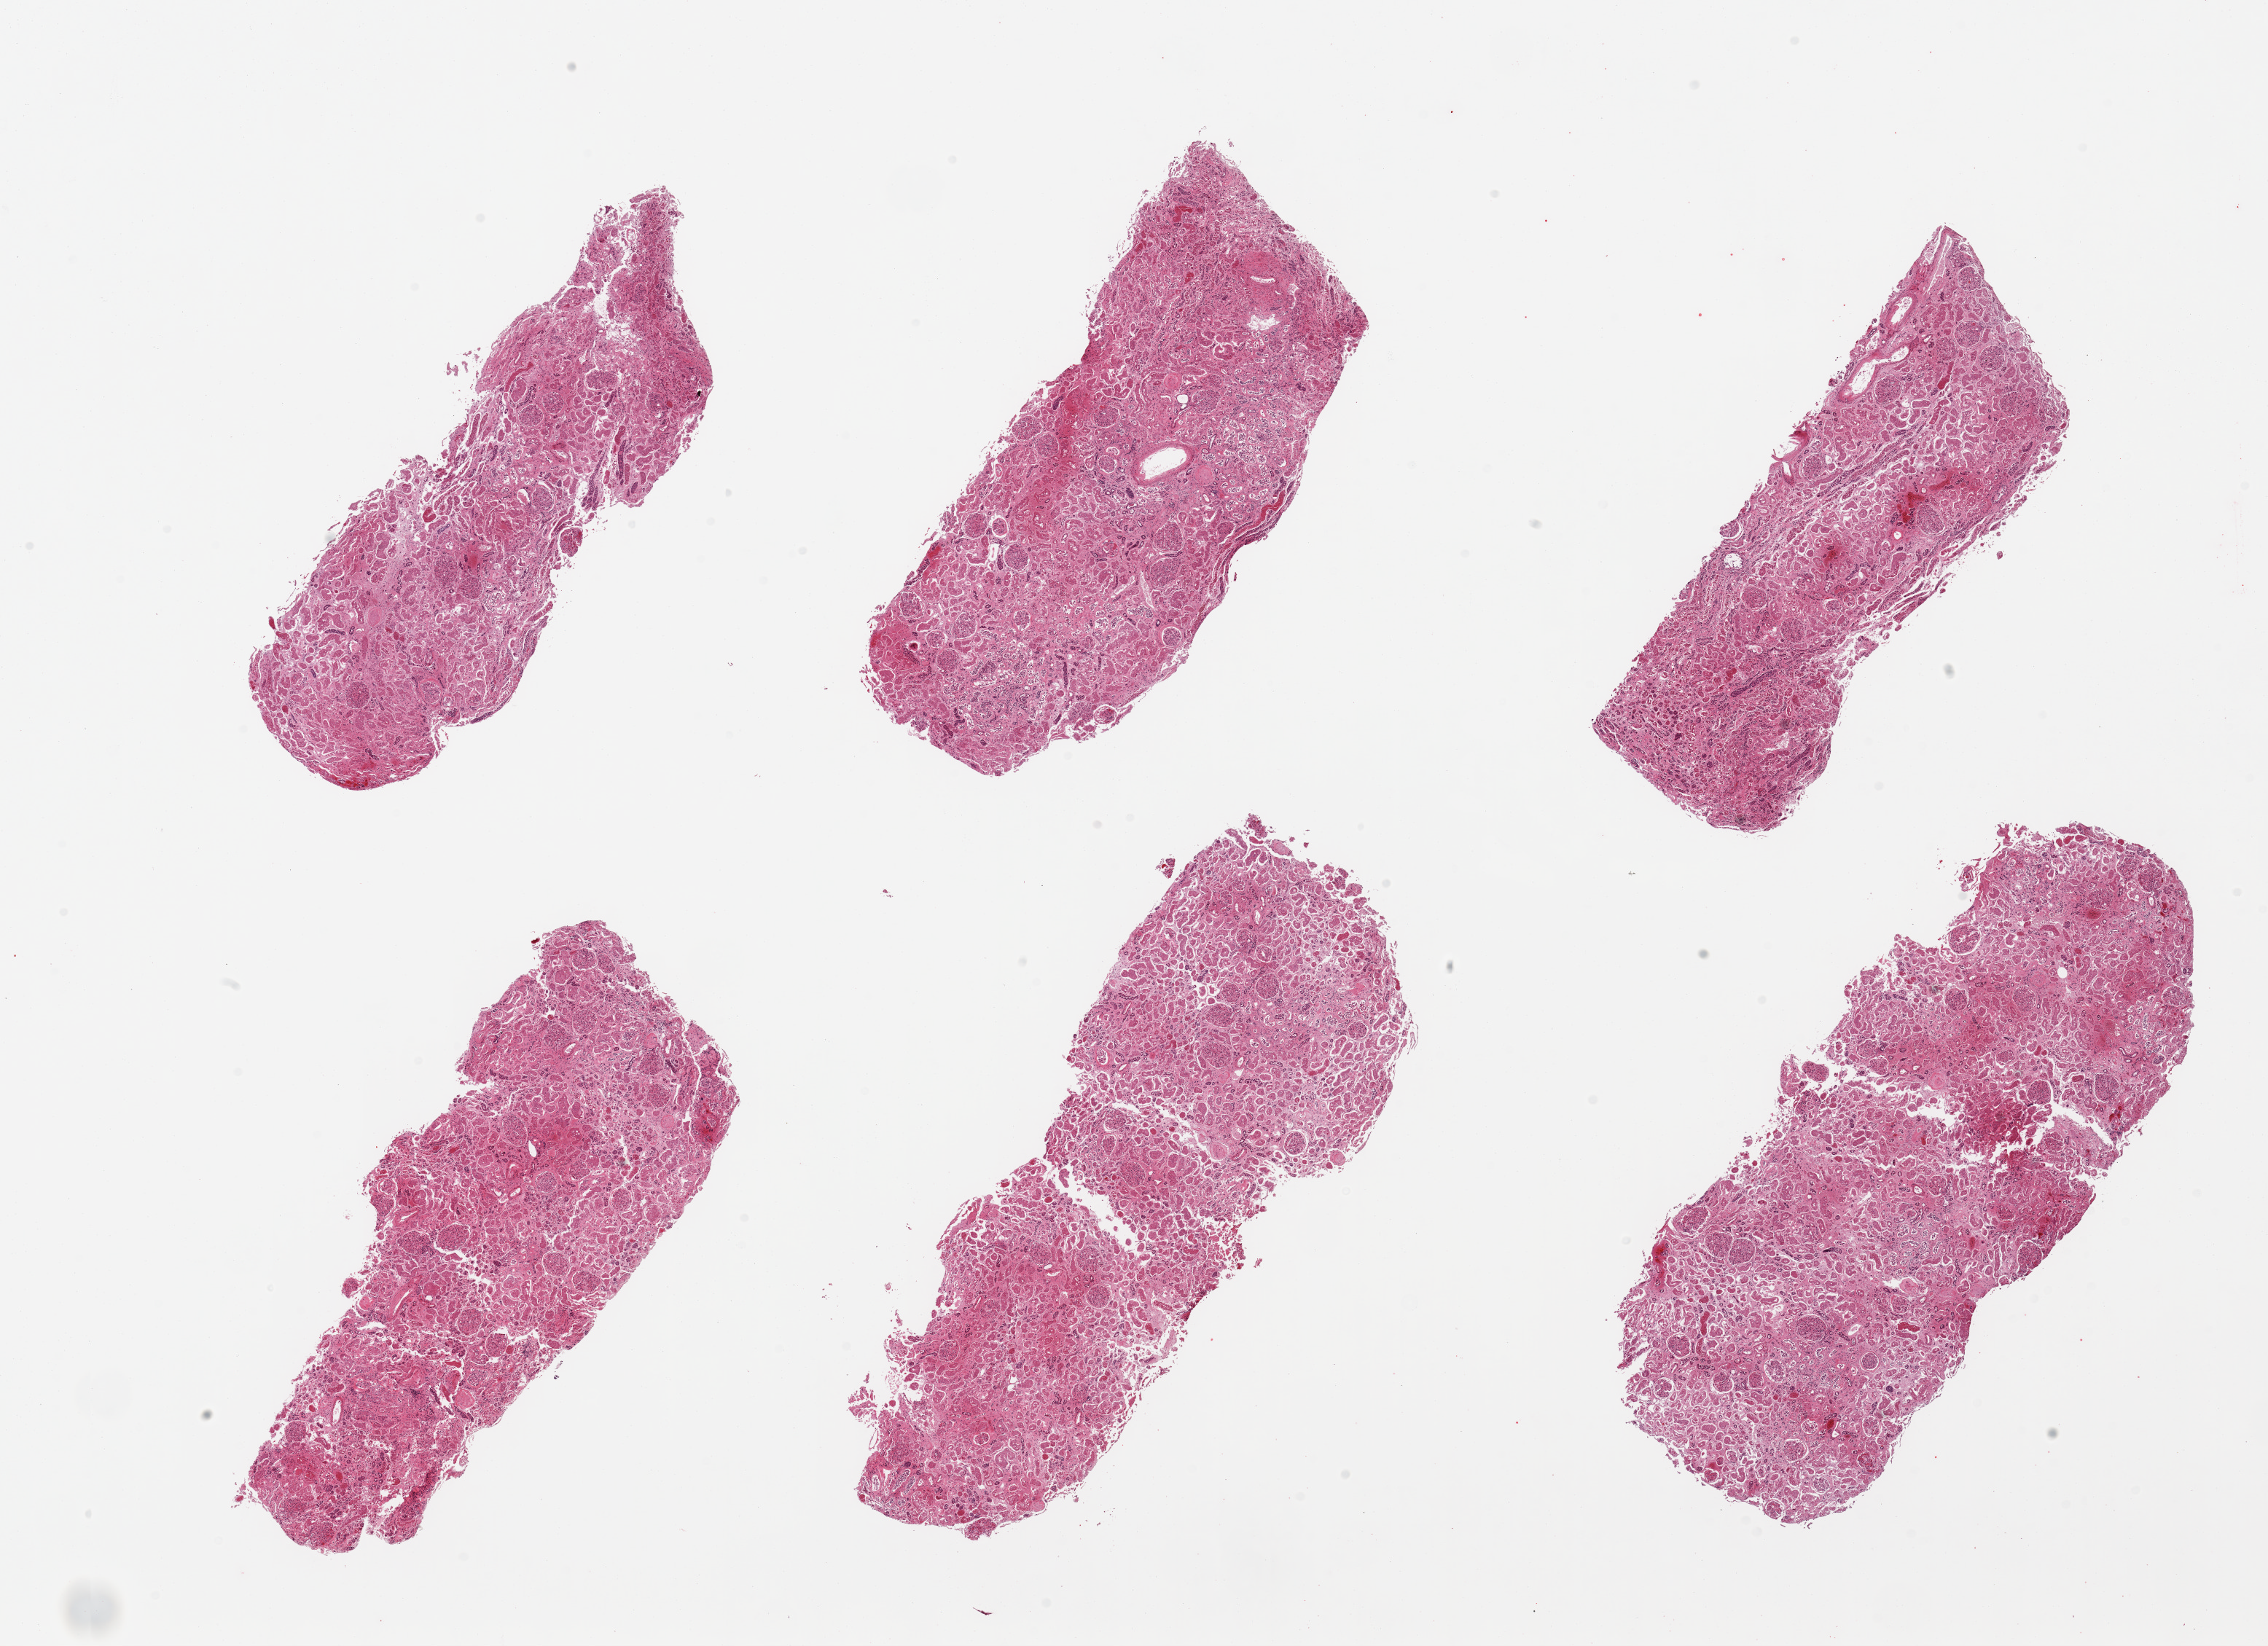
Digitized H&E-stained section, low-resolution overview of the scanned area, about 24.6 x 17.9 mm. PAXgene-fixed paraffin-embedded (PFPE) section. Sampled site (target tissue): renal cortex. Tissue donor sample. Donor sex: female.
Reviewer comment on this tissue sample: 6 pieces; tubules very autolyzed, cannot distinguish from acute tubular necrosis, scattered sclerotic glomeruli, arterio/arteroiolonephrosclerosis.